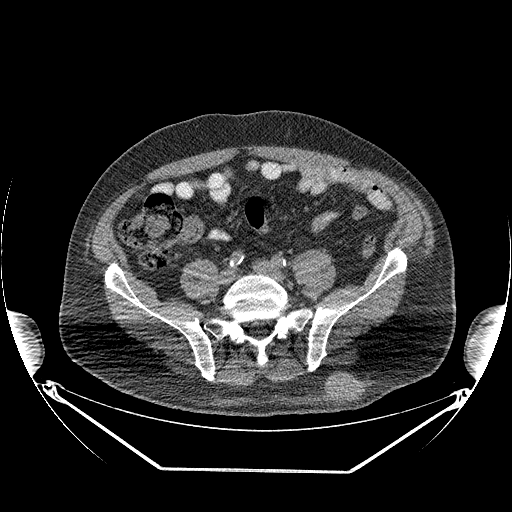
CT of an extremity soft-tissue mass (from a PET/CT study), one axial slice; position 94 of 267 along the scan axis; reconstruction kernel STANDARD; 140 kVp; soft-tissue window (W 400 / L 40 HU); 512 × 512 image matrix, field of view 500 × 500 mm. Male patient. From the clinical record (not read from this slice): histological type: pleiomorphic leiomyosarcoma; grade: high; site of the primary tumour: left buttock.
Structures marked on this image (expert contour drawn on MRI and transferred to this co-registered scan by the dataset authors):
- gross tumour volume including surrounding oedema: box from (x=324, y=374) to (x=360, y=405) px
- gross tumour volume (mass): (x=324, y=377)–(x=359, y=405)